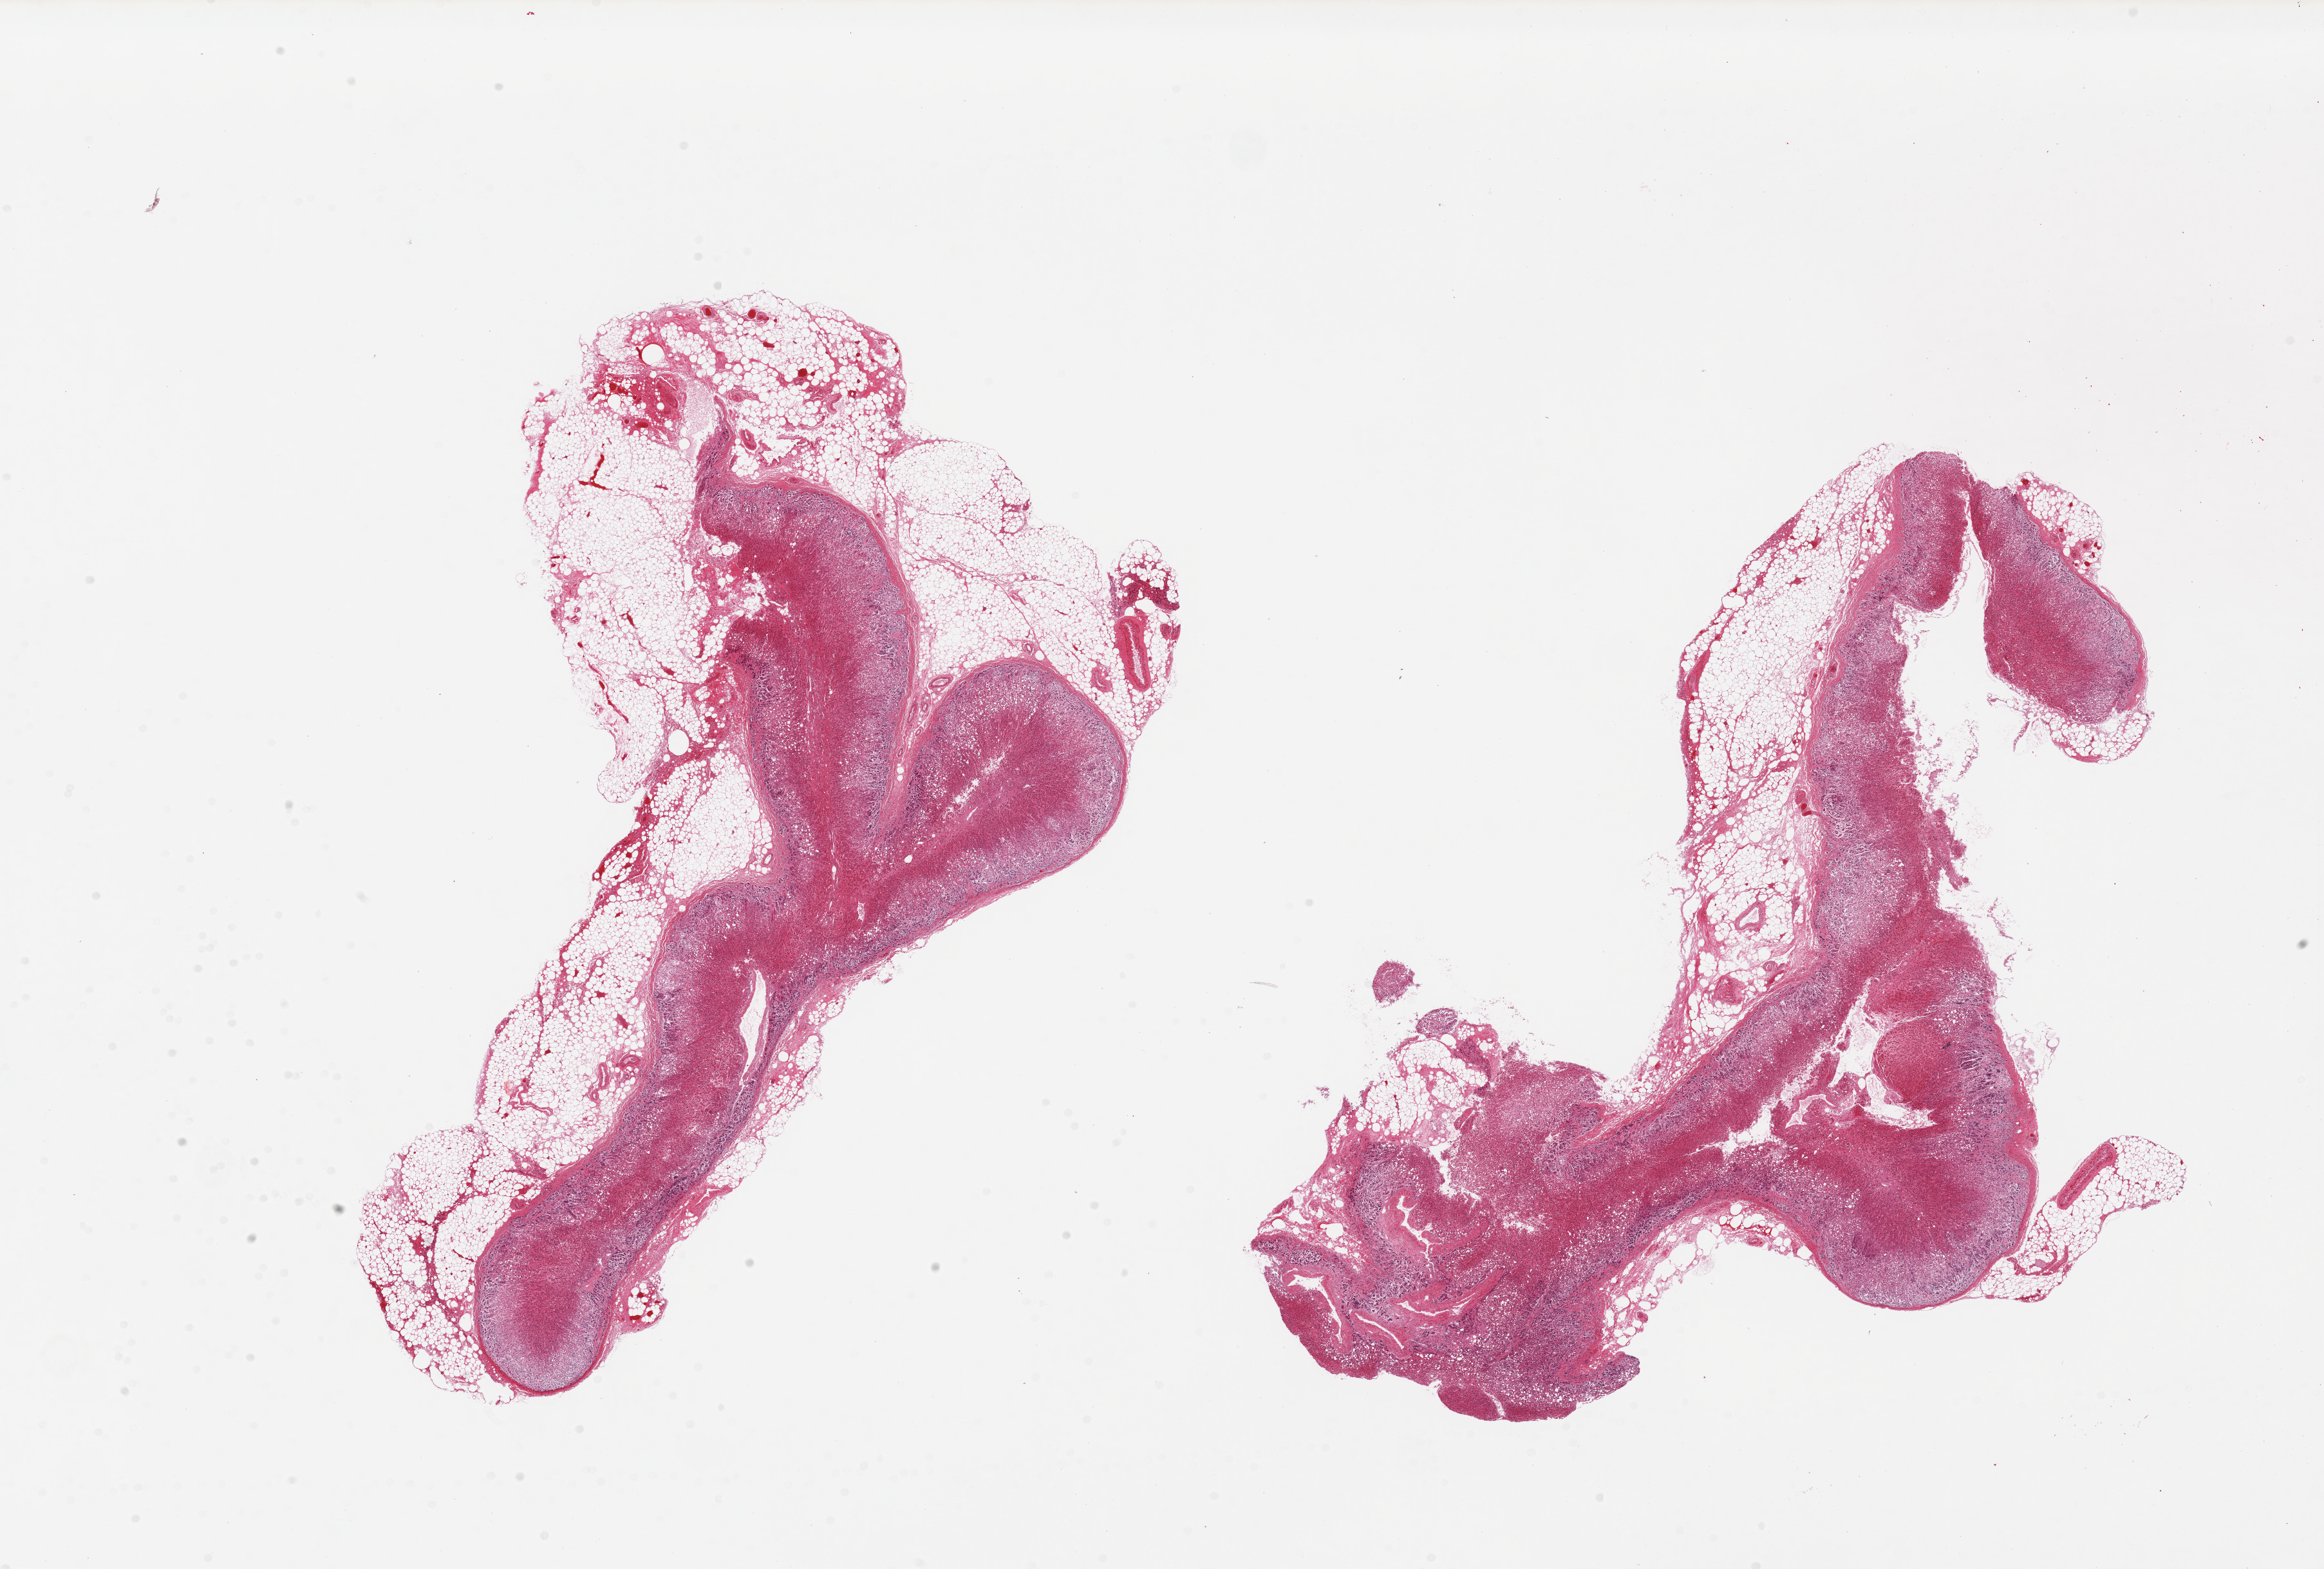
Whole-slide image, hematoxylin and eosin (H&E) stain, brightfield — shown as a low-resolution overview of the whole scanned area (about 28.5 x 19.3 mm). PAXgene-fixed paraffin-embedded (PFPE) section. Section of adrenal gland (target tissue). Donor tissue sample.
Pathologist's review note for this sample: 2 pieces. Up to 2 mm external fat.